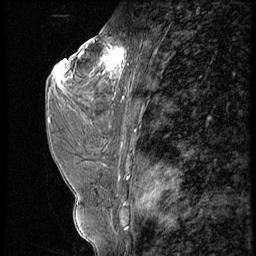
Breast MRI (dynamic contrast-enhanced), one sagittal slice. Slice 31 of 56 in the series (ordered by position). 4 images stored at this slice position (order not interpretable as contrast timing). 1.5 T. TE 4.2 ms, TR 9 ms. 2.5 mm slice thickness. 256 × 256 image matrix. Patient: female, 44 years. Case-level facts recorded for this patient, not image findings: setting: breast cancer imaged before/during neoadjuvant chemotherapy; receptor status: triple-negative.
Annotated regions visible in this slice (semi-automatically segmented with operator editing):
- analysis volume of interest (the breast-tissue region the enhancement analysis was run in; not a lesion): bounding box <87,28,132,99> (left, top, right, bottom; pixels)
- tumour enhancement mask (voxels above the 140 % enhancement threshold inside the analysis volume of interest): <93,41,127,78>